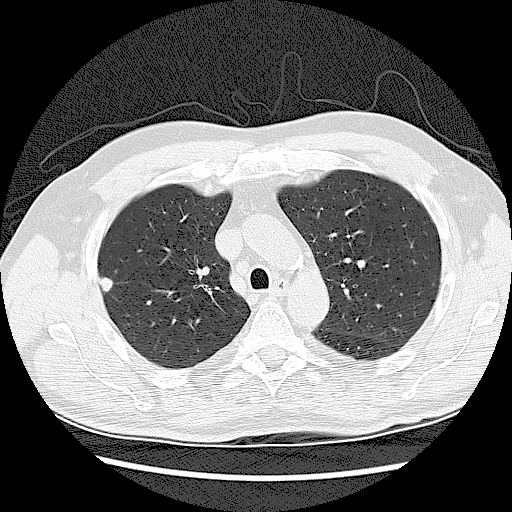
Low-dose screening chest CT, axial slice. Second annual screen. Lung window (W 1500 / L -600 HU). Lung (sharp) reconstruction kernel (LUNG). Male, age 62 years at enrolment. Former smoker at enrolment.
• Lesion marked by an expert reader, bounding box [x1, y1, x2, y2] px = [90, 271, 119, 297].
• Reader record for this screening exam (exam-level; its link to the box is not recorded): non-calcified nodule or mass ≥4 mm, right upper lobe, 10 × 10 mm, smooth margins, soft tissue attenuation, pre-existing on the prior screen: yes; interval growth: yes.
• Official screen result: positive, other.
• Participant outcome: lung cancer diagnosed 6 days after this screen — adenocarcinoma, NOS, right upper lobe, poorly differentiated (G3), stage IIB (AJCC 6th edition), 5 mm at pathology.